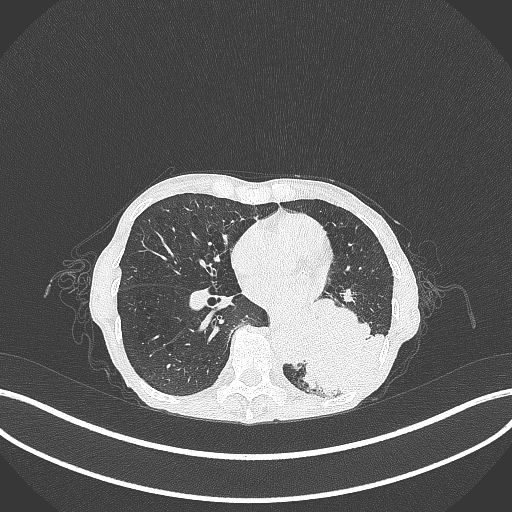
Chest CT, one axial slice; position 115 of 347 along the scan axis; lung window (W 1500 / L -600 HU); 512 × 512 image matrix, field of view 400 × 400 mm. Patient: female, 70 years. Case-level facts recorded for this patient, not image findings: clinical TNM (as recorded): T3 N0 M0; histopathological grade: G3.
Annotated regions visible in this slice (rectangle marked by the reading radiologist):
- lung tumour (recorded histology: small cell carcinoma): bounding box <291,301,393,401> (left, top, right, bottom; pixels)